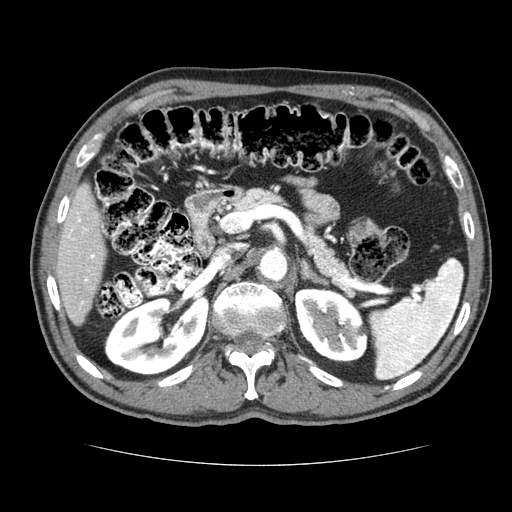
Contrast-enhanced abdominal CT (liver protocol), one axial slice. Slice 36 of 79 in the series (ordered by position). Reconstruction kernel STANDARD. 120 kVp. Soft-tissue window (W 400 / L 40 HU). 512 × 512 image matrix. From the clinical record (not read from this slice): diagnosis: hepatocellular carcinoma (patient treated with transarterial chemoembolisation; whether this scan precedes or follows treatment is not stated here); TNM stage (as recorded): Stage-I; Child-Pugh class: A.
Structures marked on this image (semi-automatic segmentation, software-assisted and operator-edited):
- liver parenchyma outside the tumour (the mass and vessels are separate outlines, so this box may not span the whole liver): bounding box <54,182,106,325> (left, top, right, bottom; pixels)
- liver vessels: <67,216,95,304>